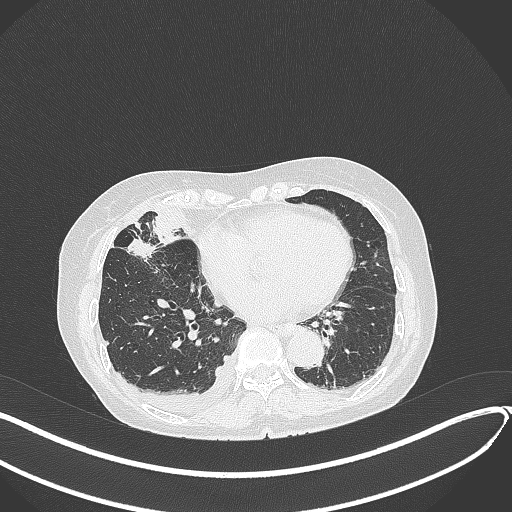
Chest CT, one axial slice. Position 145 of 418 along the scan axis. Lung window (W 1500 / L -600 HU). 1 mm slice thickness. 512 × 512 image matrix. Patient: female, 75 years. From the clinical record (not read from this slice): clinical TNM (as recorded): T2a N3 M0.
Outlined on this slice (rectangle marked by the reading radiologist):
- lung tumour (recorded histology: adenocarcinoma): box from (x=124, y=235) to (x=161, y=266) px